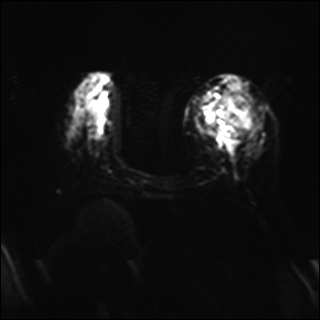
Breast MRI, one axial slice; position 12 of 37 along the scan axis; diffusion-weighted series; image 2 of 4 stored at this slice position (different b-values; order by instance number); 1.5 T; 4 mm slice thickness; 320 × 320 image matrix. Female patient.
Annotated regions visible in this slice (outlined manually by an expert reader):
- tumour on diffusion-weighted imaging: bounding box [x1, y1, x2, y2] px = [218, 92, 260, 139]